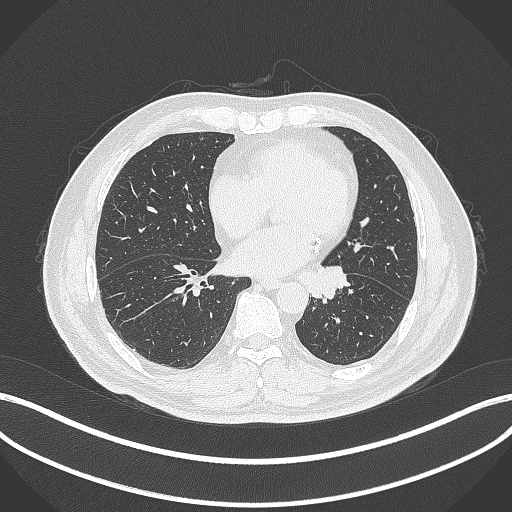
Chest CT, one axial slice. Slice 113 of 312 in the series (ordered by position). Reconstruction kernel B70f. Lung window (W 1500 / L -600 HU). 512 × 512 image matrix, field of view 400 × 400 mm. Patient: male, 71 years. Case-level facts recorded for this patient, not image findings: clinical TNM (as recorded): T1b N0 M0.
Outlined on this slice (bounding box drawn by a radiologist):
- lung tumour (recorded histology: squamous cell carcinoma): bounding box [x1, y1, x2, y2] px = [296, 265, 352, 301]